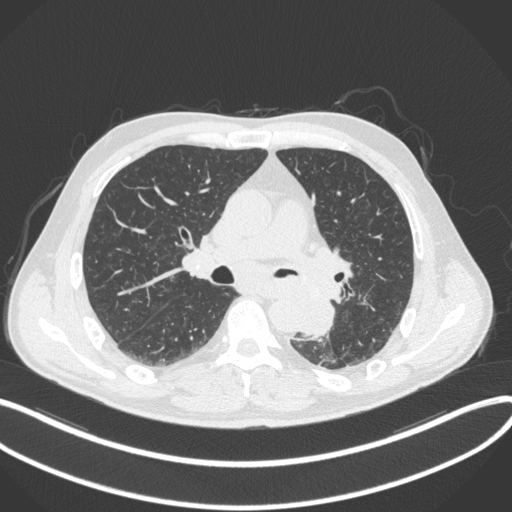
Chest CT, one axial slice. Position 201 of 328 along the scan axis. Reconstruction kernel B31f. Lung window (W 1500 / L -600 HU). 1 mm slice thickness. 512 × 512 image matrix, field of view 400 × 400 mm. Patient: male, 59 years. Case-level facts recorded for this patient, not image findings: clinical TNM (as recorded): T2a N2 M0.
Structures marked on this image (rectangle marked by the reading radiologist):
- lung tumour (recorded histology: squamous cell carcinoma): bounding box (x1, y1, x2, y2) in pixels: (293, 284, 337, 345)